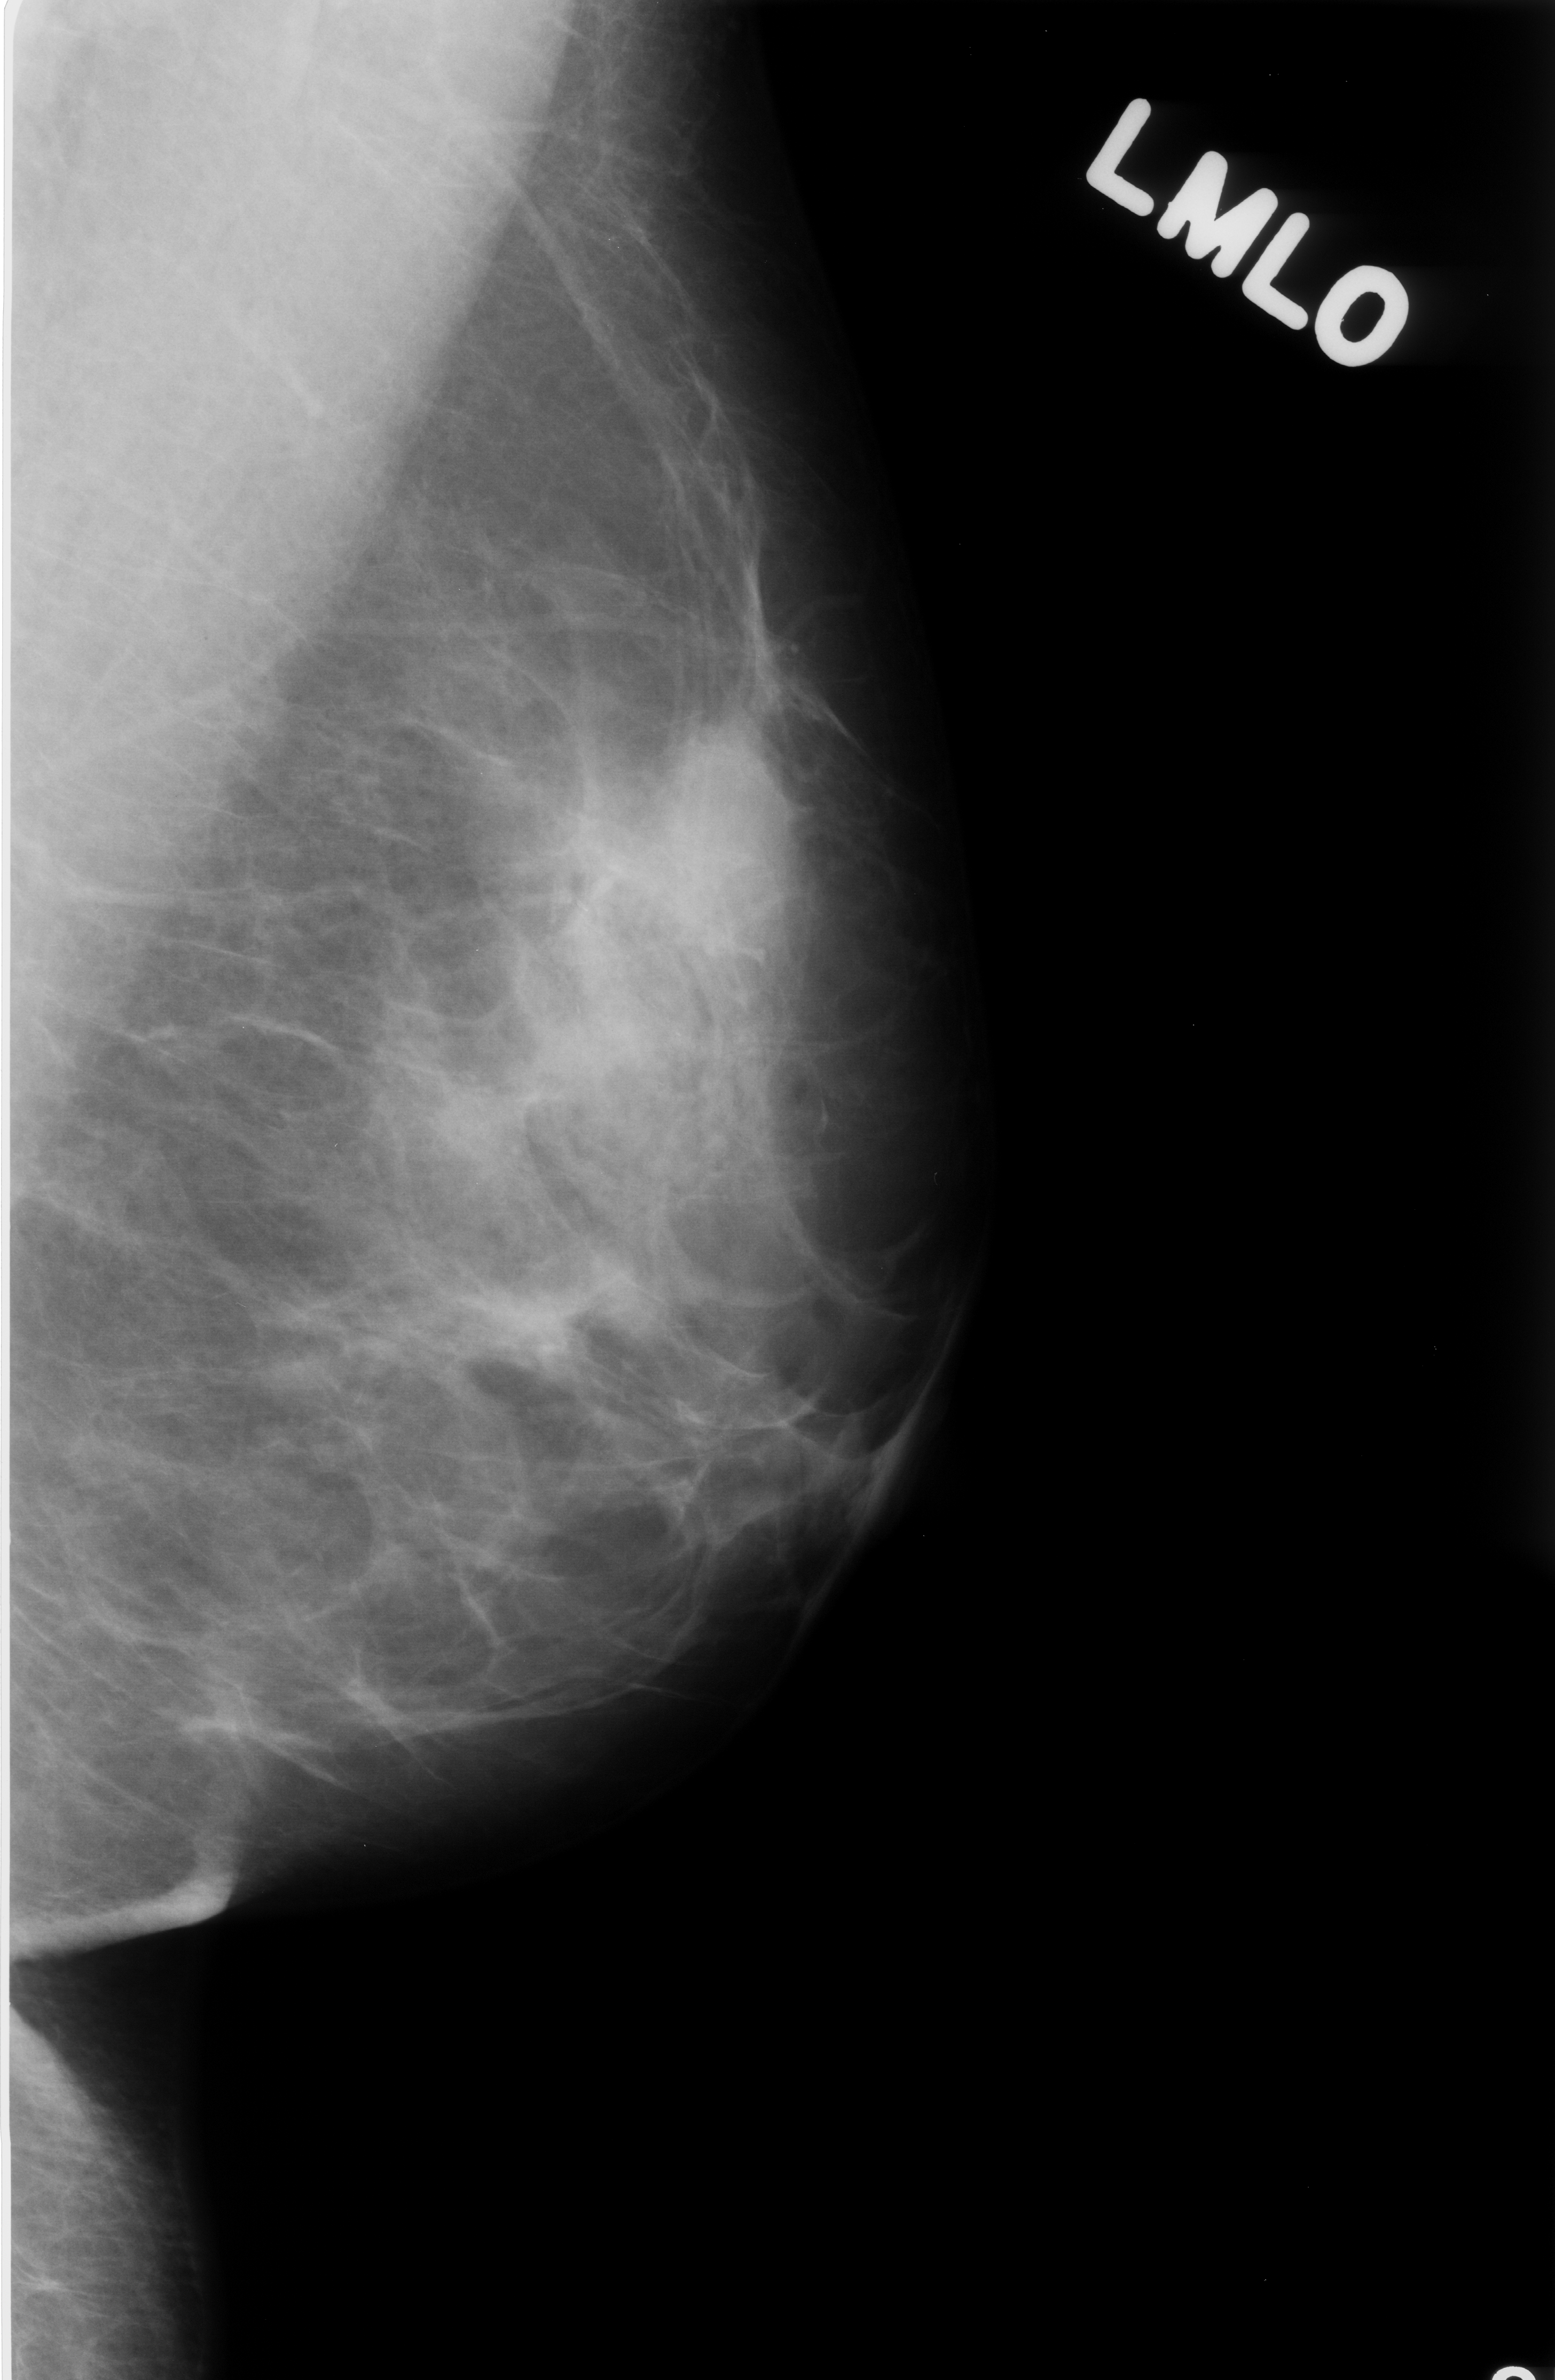
Digitized screen-film mammogram; left breast; MLO view; breast composition: scattered fibroglandular densities (BI-RADS density category 2 of 4).
Finding: calcifications, morphology fine linear branching, distribution linear; BI-RADS assessment category 4; pathology result (as recorded, not read from the image): benign.